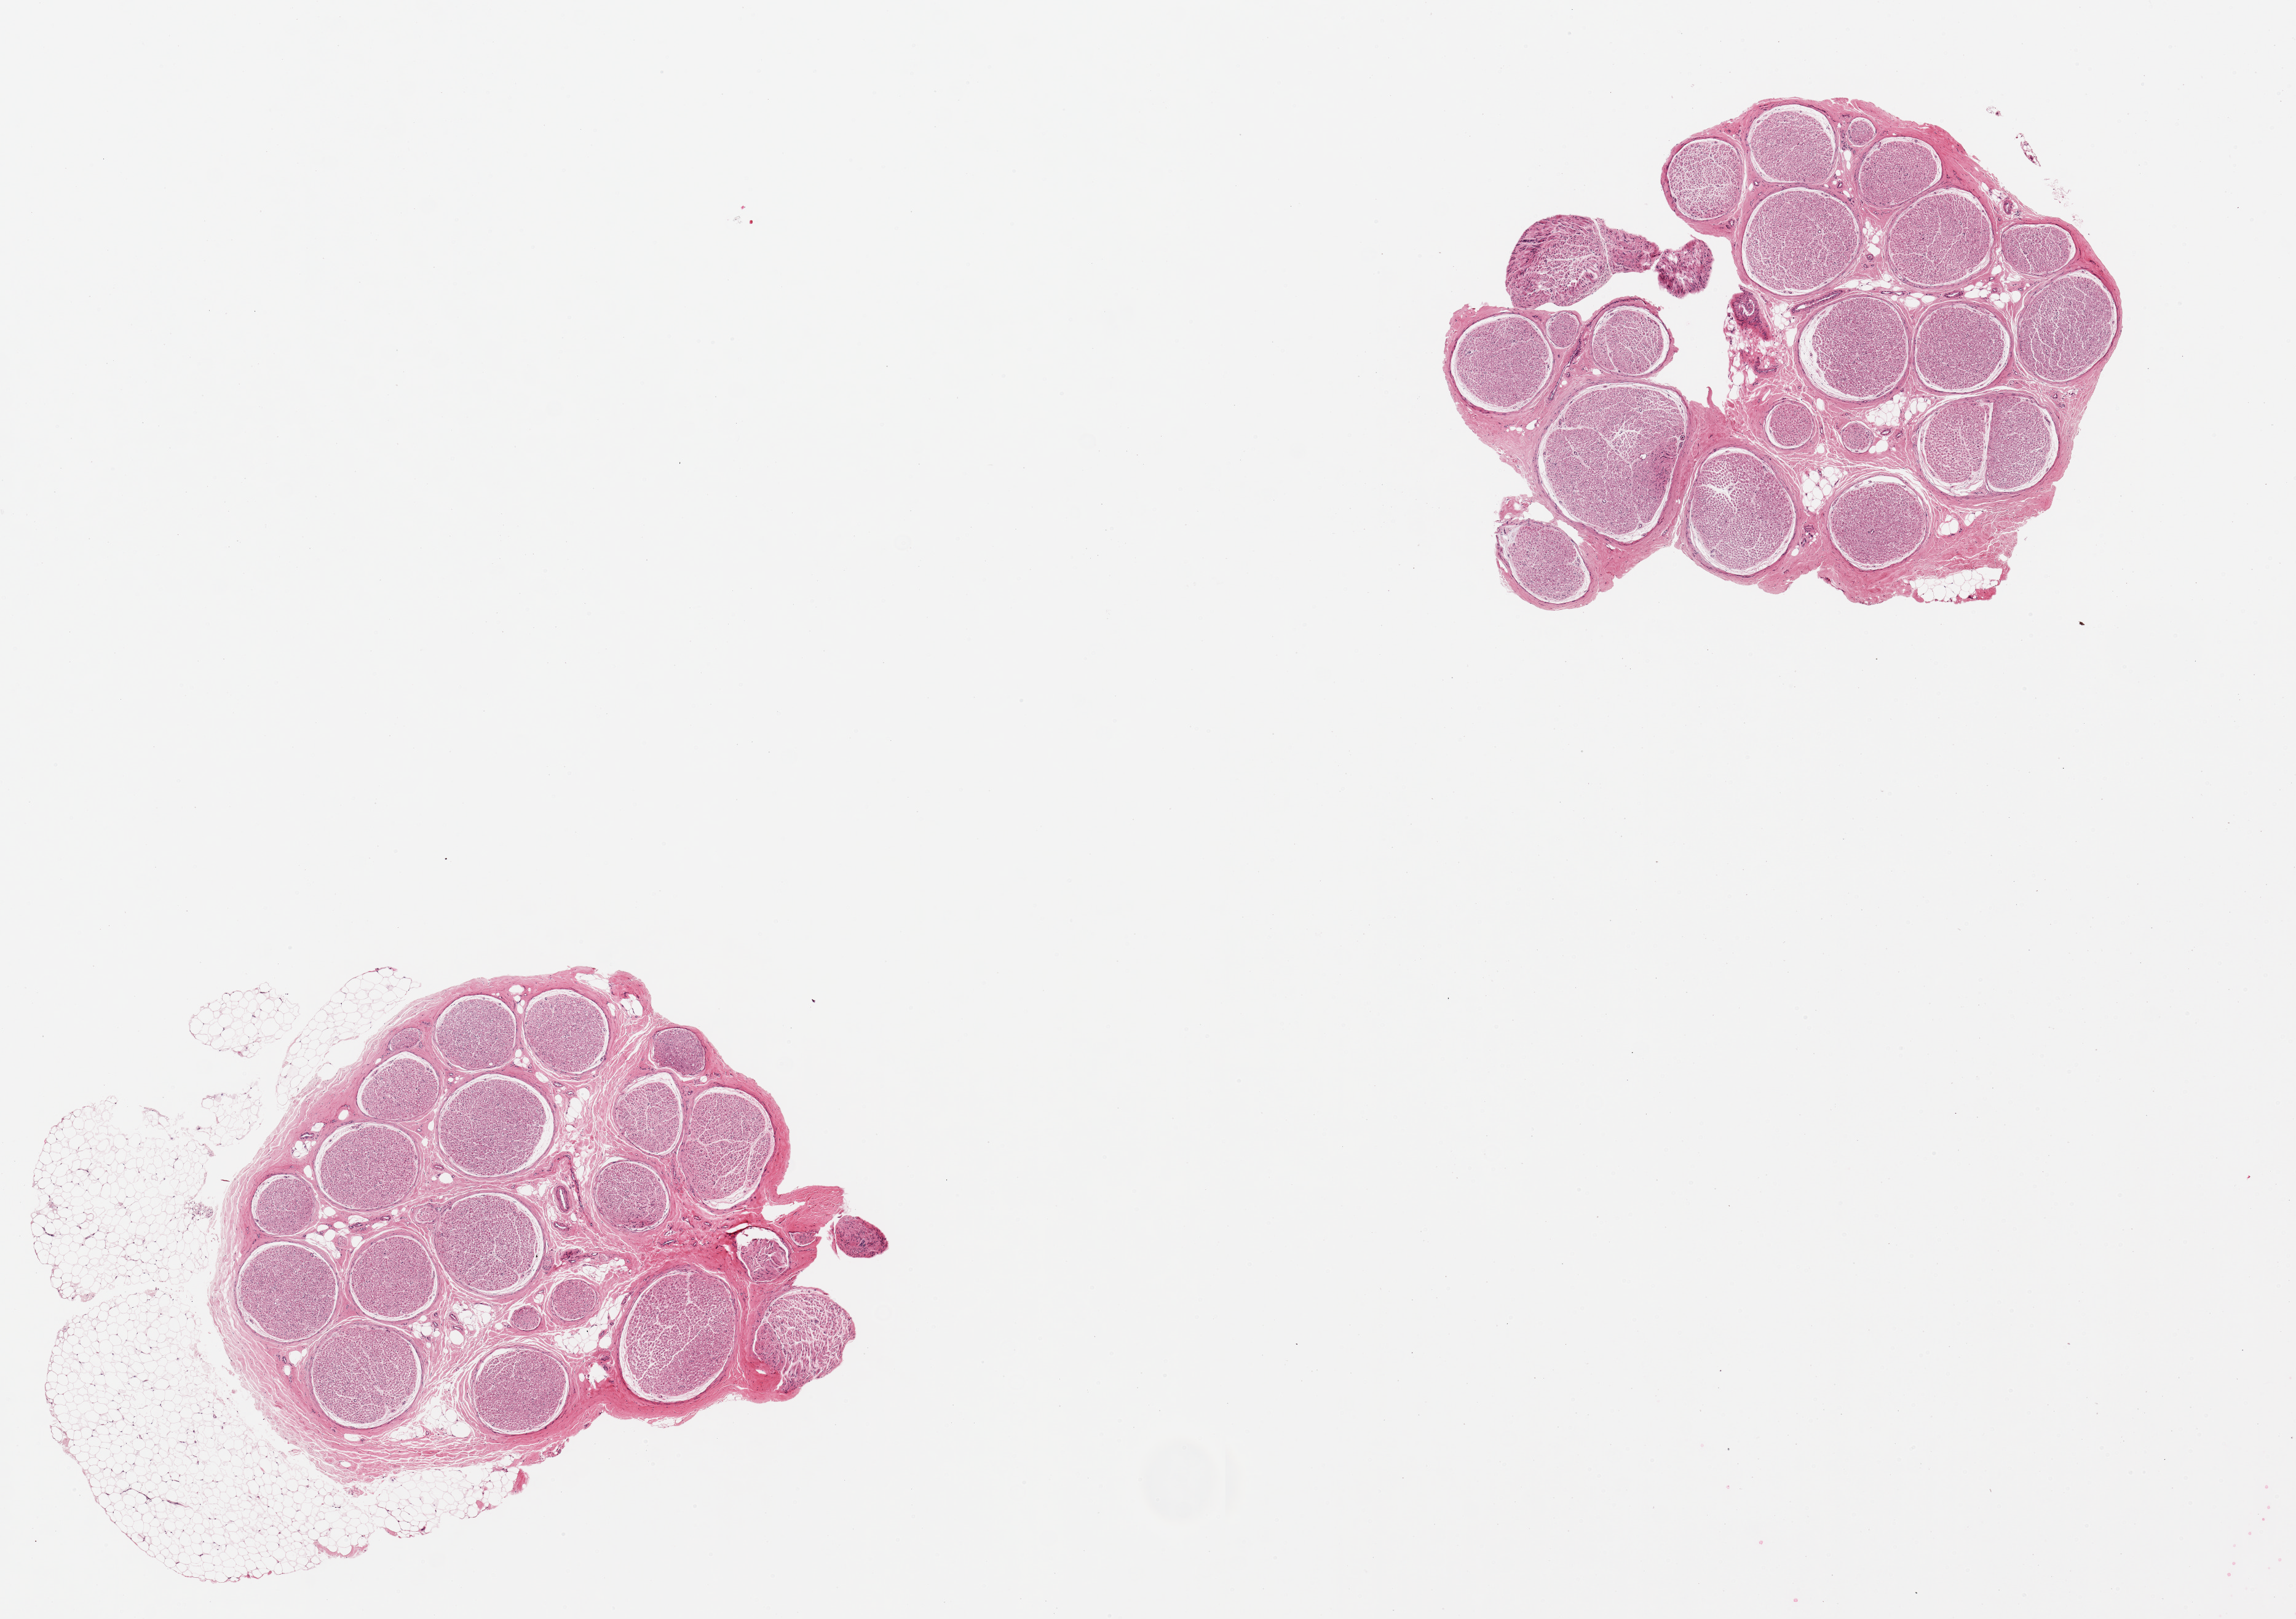
Whole-slide image, haematoxylin and eosin stain, shown as a low-resolution overview of the whole scanned area (about 14.8 x 10.4 mm, from a 20x scan). PAXgene-fixed, paraffin-embedded tissue. Sampled site (target tissue): tibial nerve. Donor tissue sample.
Pathologist's review note for this sample: 2 pieces, adherent ~1mm nubbin/rim of fat on one but good specimens generally.